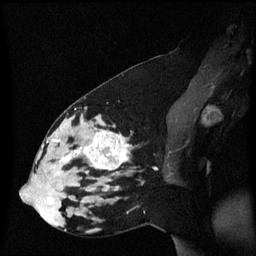
Breast MRI (dynamic contrast-enhanced), one sagittal slice. Slice 27 of 60 in the series (ordered by position). Dynamic contrast-enhanced series, image 2 of 3 at this slice position (ordered by acquisition). 1.5 T. TE 4.2 ms, TR 8.4 ms. 2 mm slice thickness. 256 × 256 image matrix. Patient: female, 33 years. Case-level facts recorded for this patient, not image findings: setting: breast cancer imaged before/during neoadjuvant chemotherapy; receptor status: triple-negative.
Structures marked on this image (semi-automatic segmentation, software-assisted and operator-edited):
- analysis volume of interest (the breast-tissue region the enhancement analysis was run in; not a lesion): bounding box (x1, y1, x2, y2) in pixels: (44, 123, 139, 189)
- tumour enhancement mask (voxels above the 70 % enhancement threshold inside the analysis volume of interest): (54, 131, 129, 170)